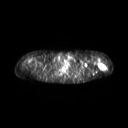
FDG PET of an extremity soft-tissue mass (from a PET/CT study), one axial slice. Slice 208 of 267 in the series (ordered by position). 128 × 128 image matrix, field of view 600 × 600 mm. Female patient, age 28 years. From the clinical record (not read from this slice): histological type: malignant fibrous histiocytoma; grade: low; site of the primary tumour: left arm.
Outlined on this slice (expert contour drawn on MRI and transferred to this co-registered scan by the dataset authors):
- gross tumour volume (mass): bounding box [x1, y1, x2, y2] px = [98, 62, 107, 70]